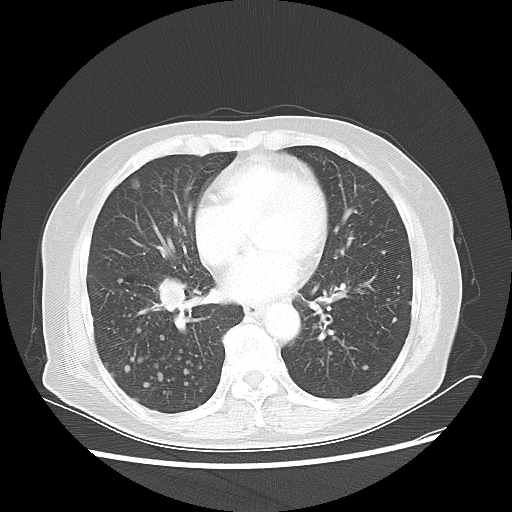
Chest CT, one axial slice. Position 23 of 56 along the scan axis. Lung window (W 1500 / L -600 HU). 512 × 512 image matrix, field of view 360 × 360 mm. Female patient, age 68 years. From the clinical record (not read from this slice): clinical TNM (as recorded): T1c N3 M0.
Outlined on this slice (rectangle marked by the reading radiologist):
- lung tumour (recorded histology: squamous cell carcinoma): bounding box (x1, y1, x2, y2) in pixels: (153, 270, 201, 315)